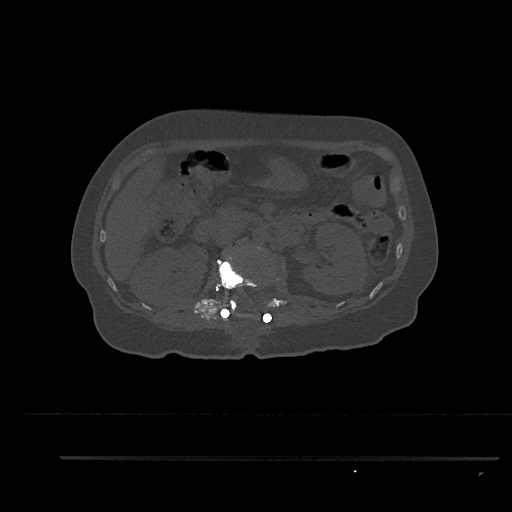
CT including the spine, one axial slice; slice 196 of 797 in the series (ordered by position); bone window (W 1800 / L 400 HU); 0.5 mm slice thickness; 512 × 512 image matrix. Female patient, age 44 years. From the clinical record (not read from this slice): primary cancer: renal.
Outlined on this slice (semi-automatic segmentation, software-assisted and operator-edited):
- L1 vertebra: bounding box [x1, y1, x2, y2] px = [218, 257, 279, 317]
- L2 vertebra: [224, 246, 262, 315]